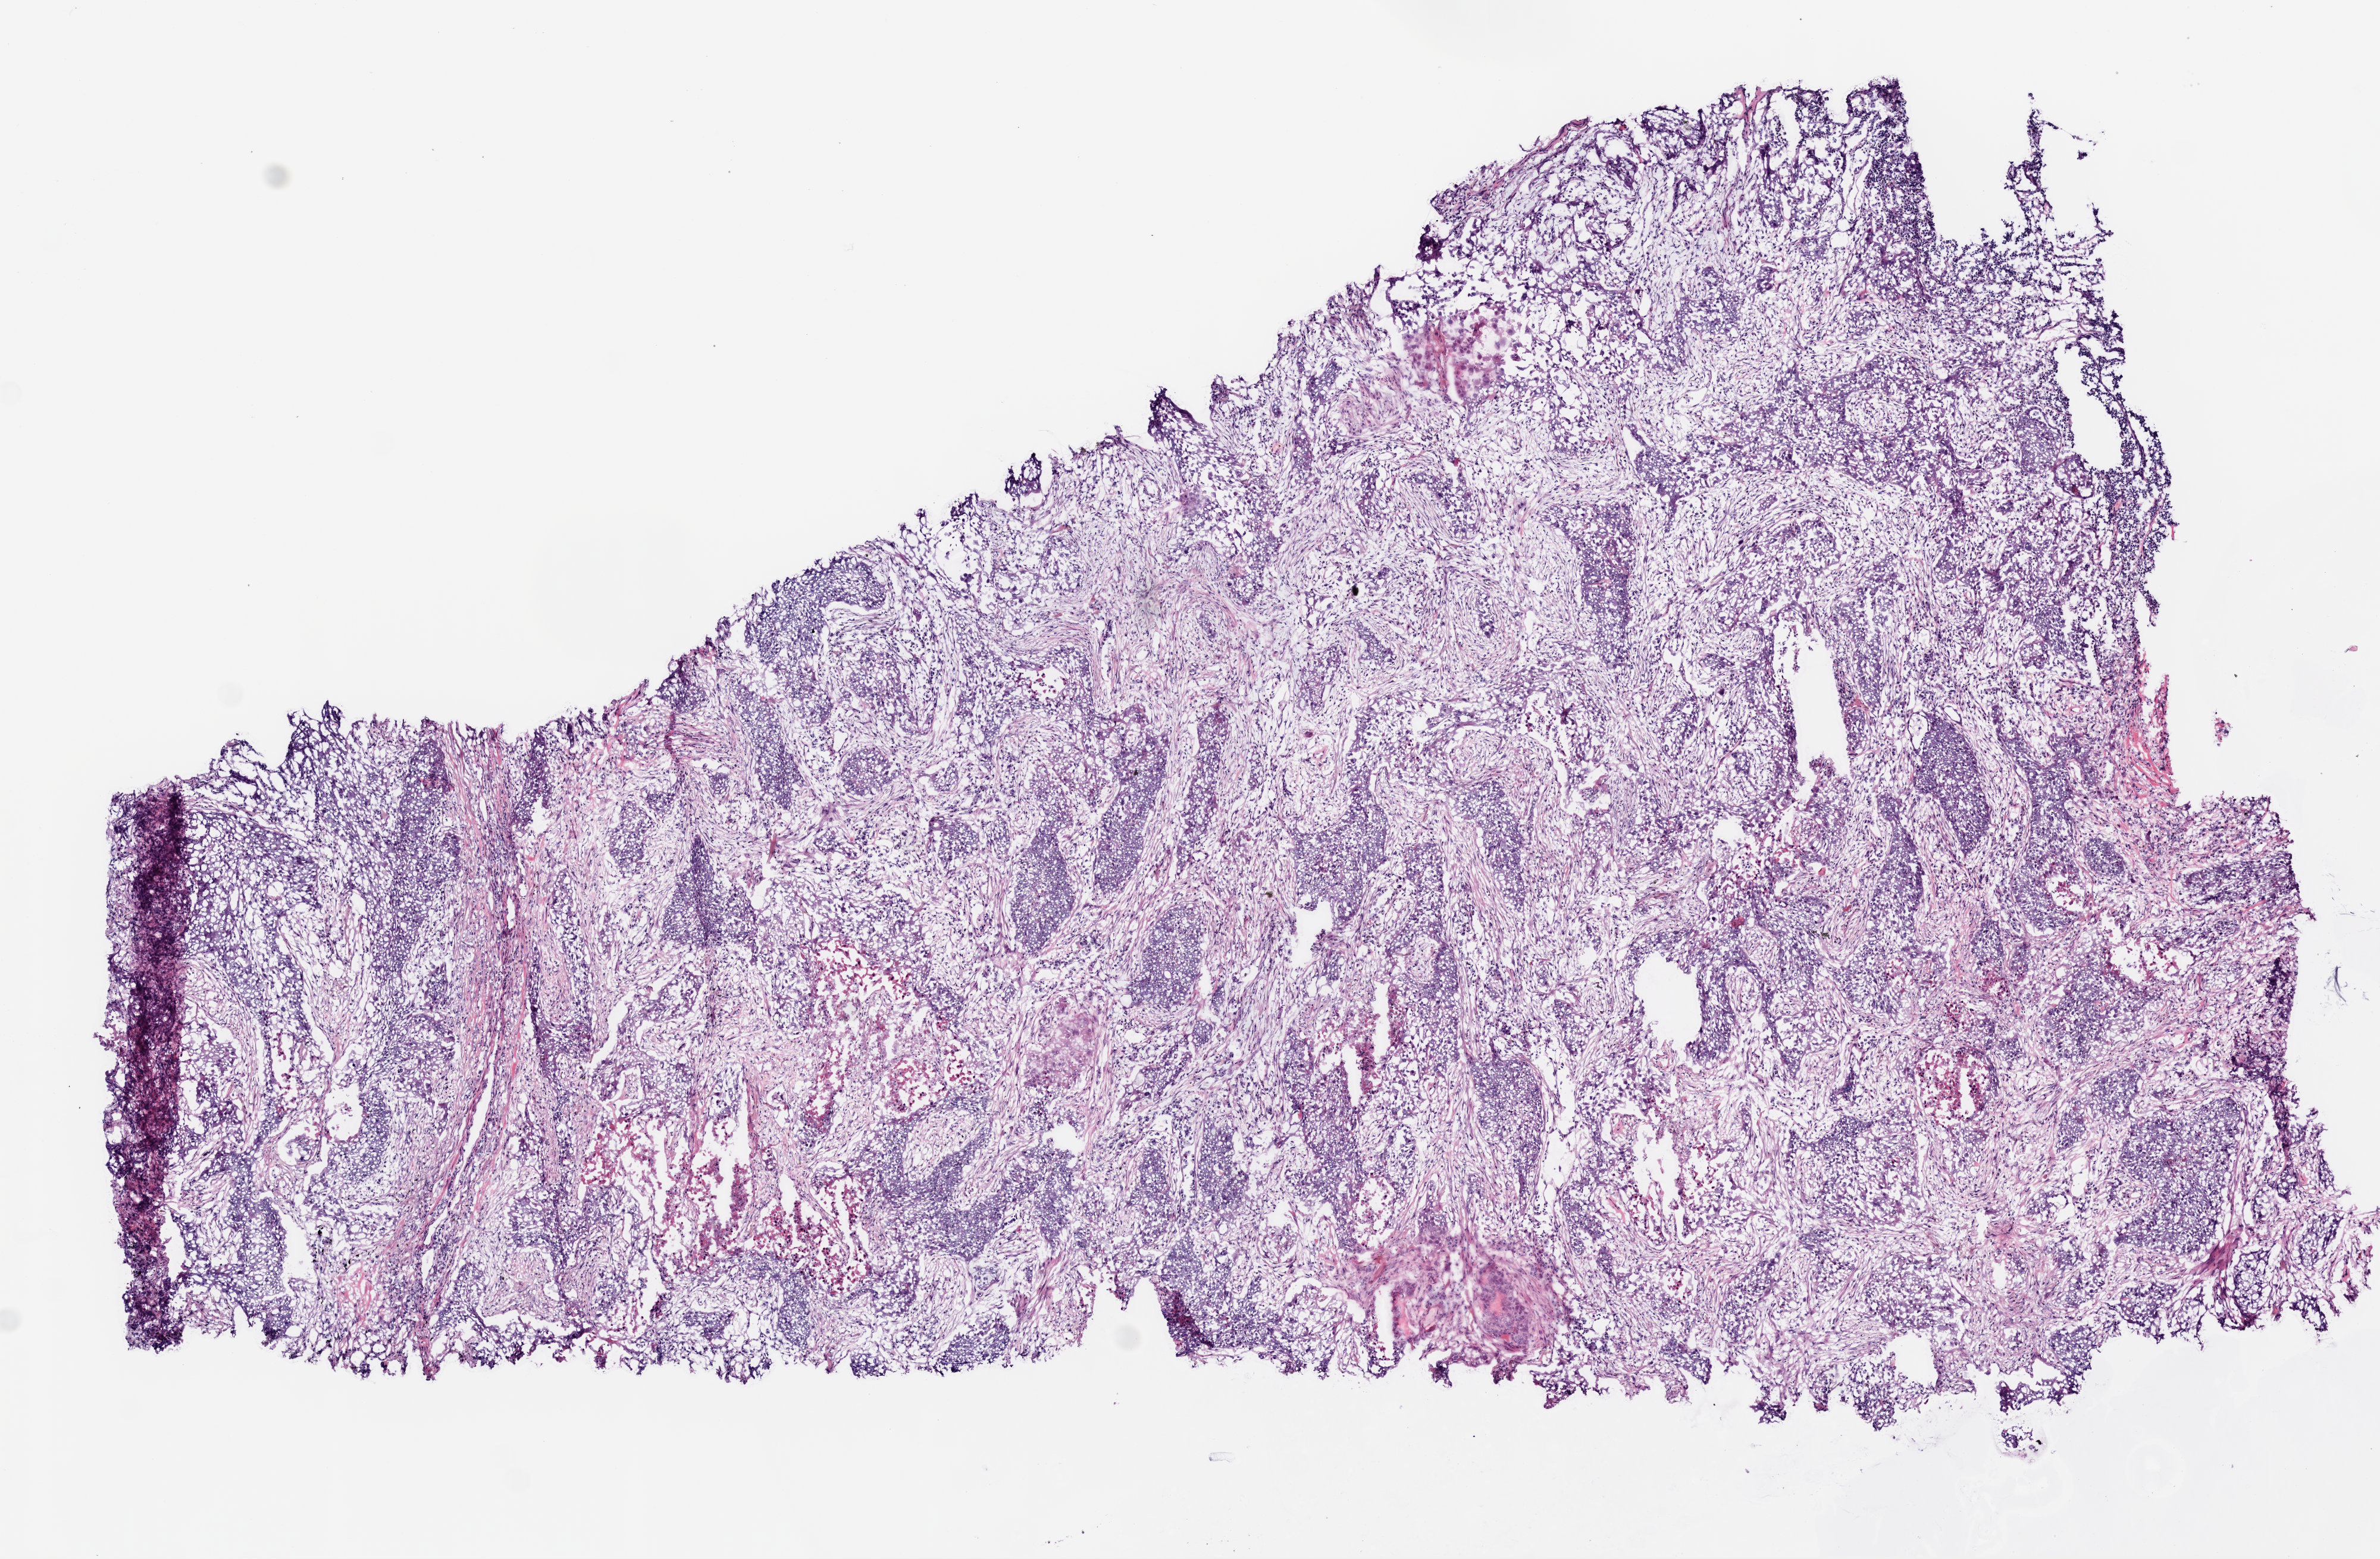
H&E-stained whole-slide image — shown as a low-resolution overview of the whole scanned area (about 8.0 x 5.3 mm); frozen section; lung, primary tumour sample. Male patient; age at initial diagnosis 65 years. Pathologist review of this section (percent, as recorded): tumour cells 40%, tumour nuclei 60%, normal cells 0%, stromal cells 45%, necrosis 15%. Inflammatory infiltration, as recorded: lymphocyte infiltration 2%.
Diagnosis: Squamous cell carcinoma, NOS. AJCC pathologic stage: IV. Laterality: right.